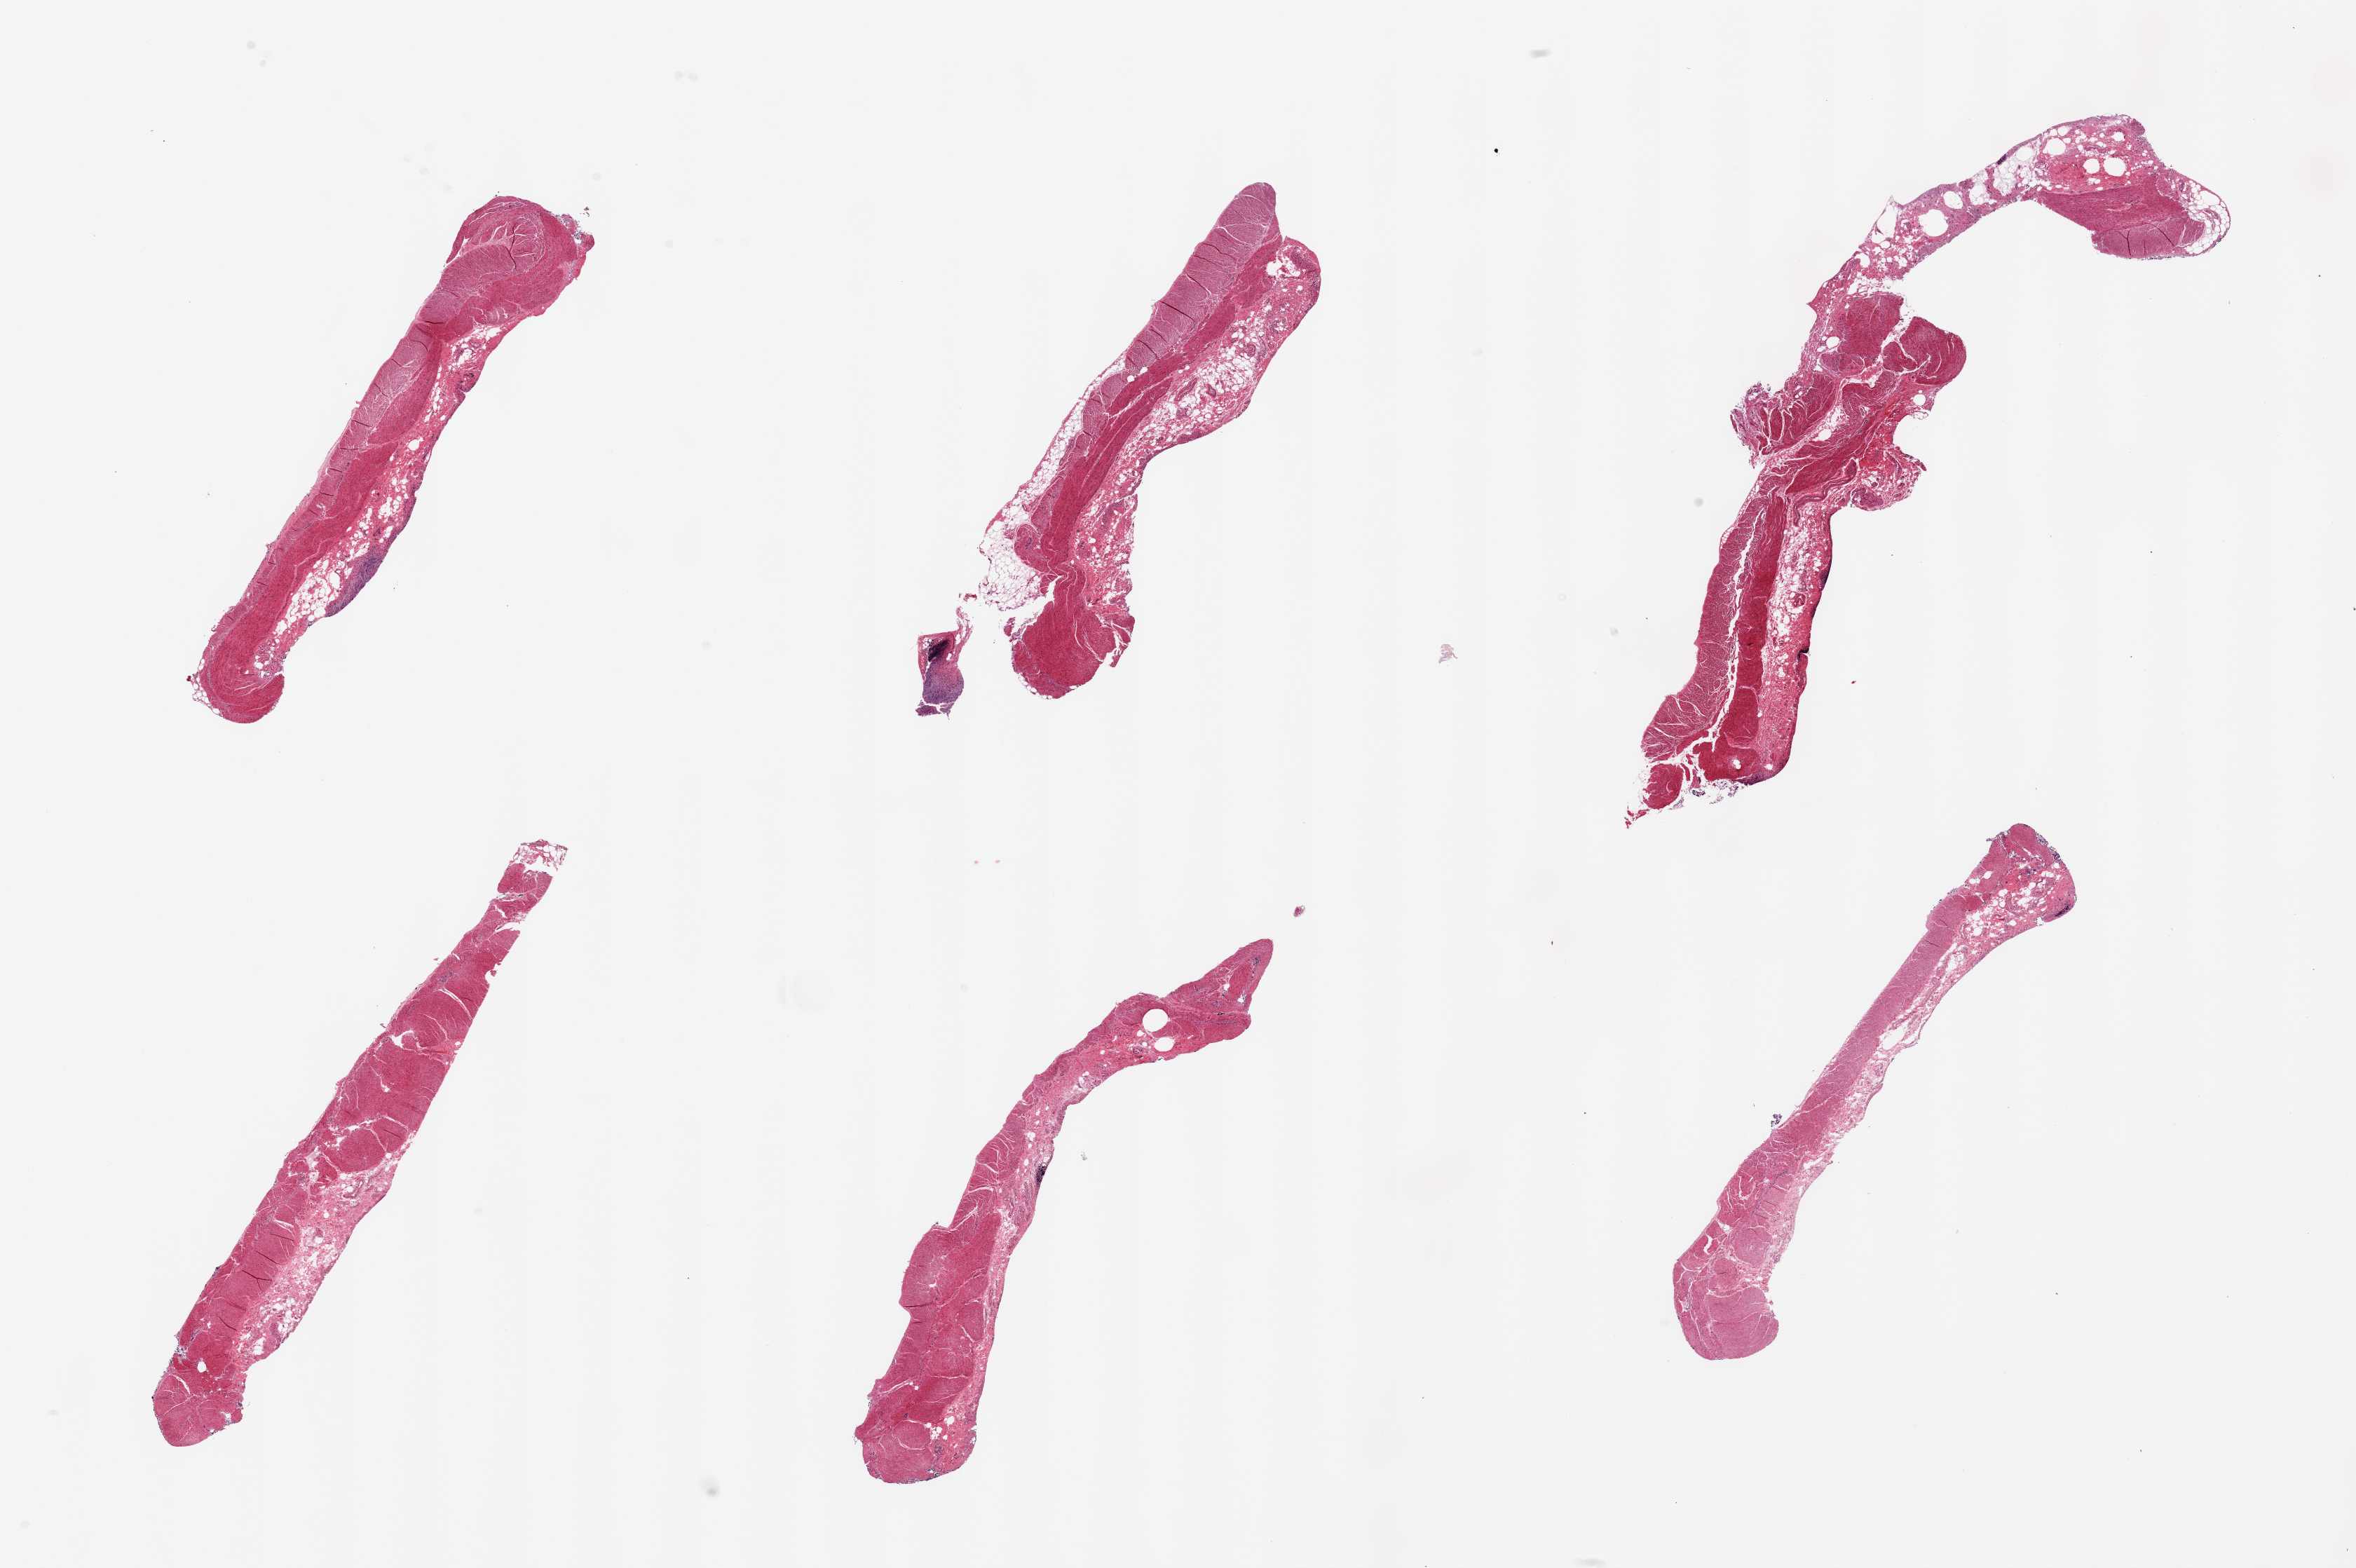
Digitized hematoxylin and eosin (H&E)-stained section, shown as a low-resolution overview of the whole scanned area (about 26.6 x 17.7 mm, slide scanned at 20x); PAXgene-fixed, paraffin-embedded tissue; target tissue: sigmoid colon; tissue donor sample.
- reviewer comment on this tissue sample: 6 pieces; submucosal fat comprises up to 40% of area